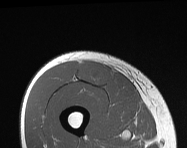
MRI of an extremity soft-tissue mass, one axial slice. Slice 49 of 114 in the series (ordered by position). MR volume resampled by the dataset authors to the PET/CT grid (not the native acquisition matrix). 3.27 mm slice thickness. 187 × 148 image matrix, field of view 183 × 145 mm. Male patient. Case-level facts recorded for this patient, not image findings: histological type: pleiomorphic leiomyosarcoma; grade: intermediate; site of the primary tumour: right thigh.
Outlined on this slice (expert contour drawn on MRI and transferred to this co-registered scan by the dataset authors):
- gross tumour volume including surrounding oedema: bounding box (x1, y1, x2, y2) in pixels: (77, 61, 110, 85)